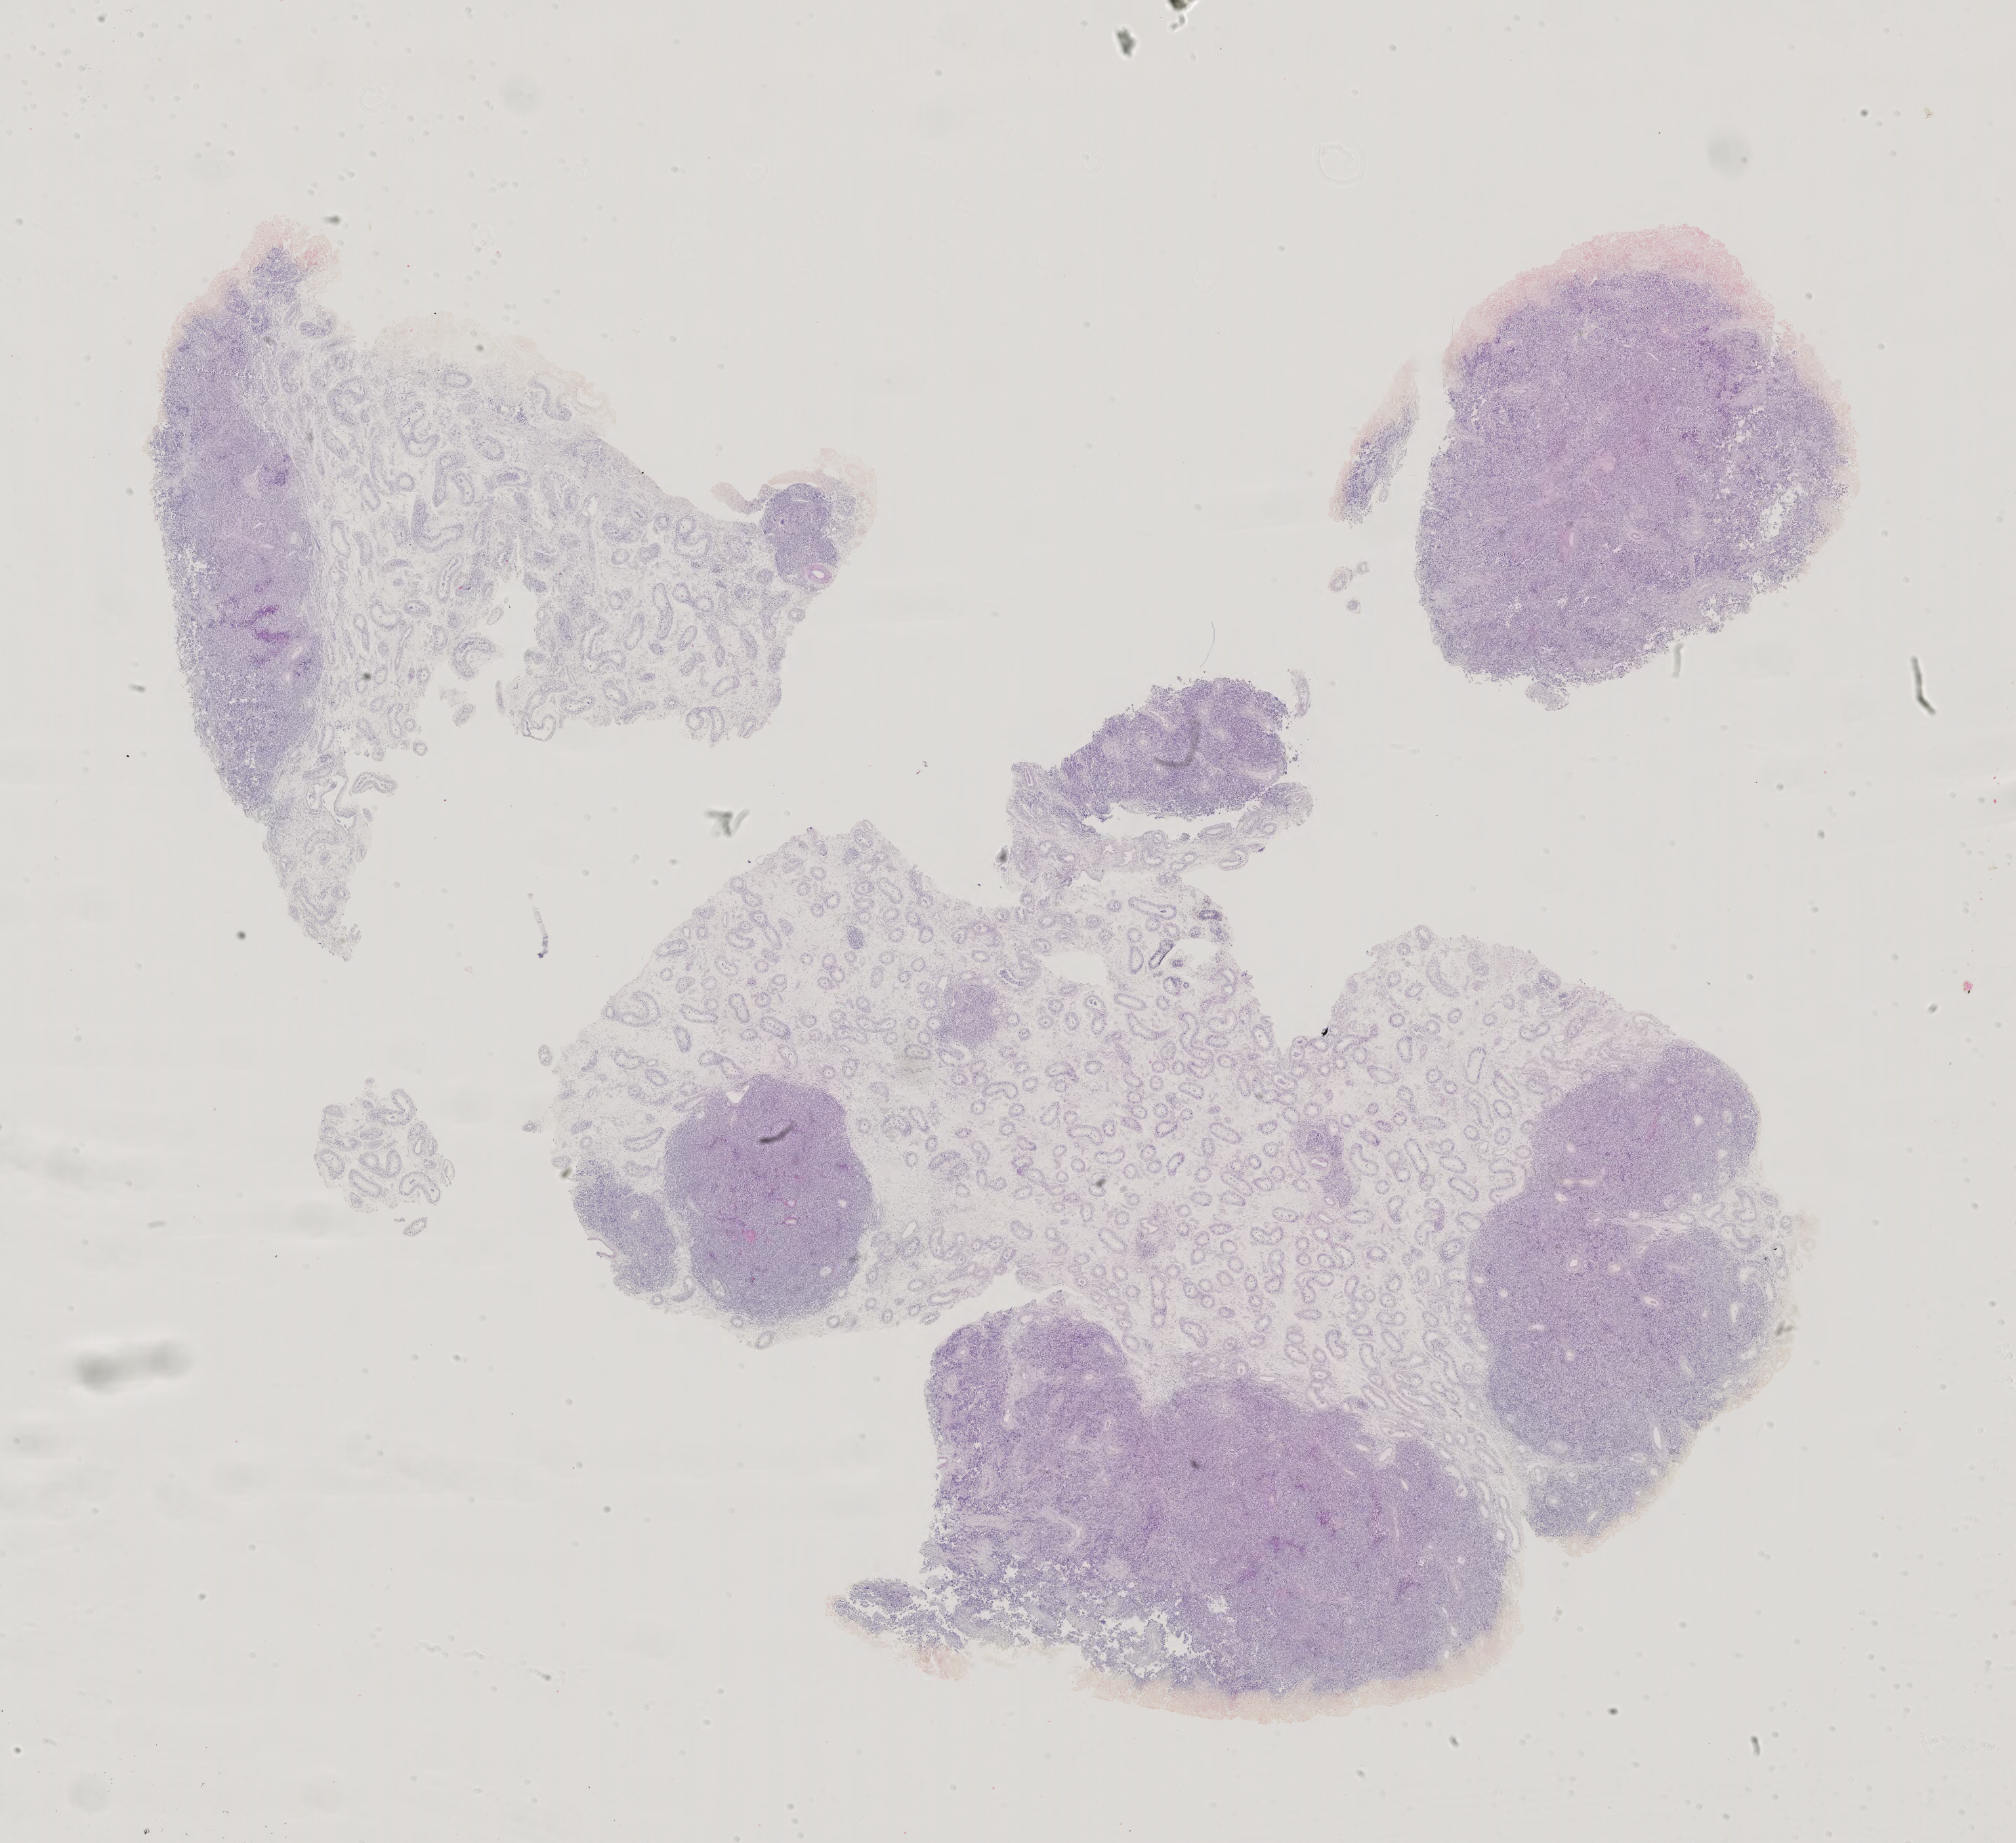
H&E whole-slide image — whole scanned area (about 22.4 x 20.5 mm, acquisition: 40x scan) shown as a low-resolution overview. Formalin-fixed paraffin-embedded (FFPE) diagnostic section. Testis, primary tumour sample. Male, age 26 years at initial diagnosis.
• histologic diagnosis: Seminoma, NOS
• TNM: T2 N0 M0
• AJCC pathologic stage: I